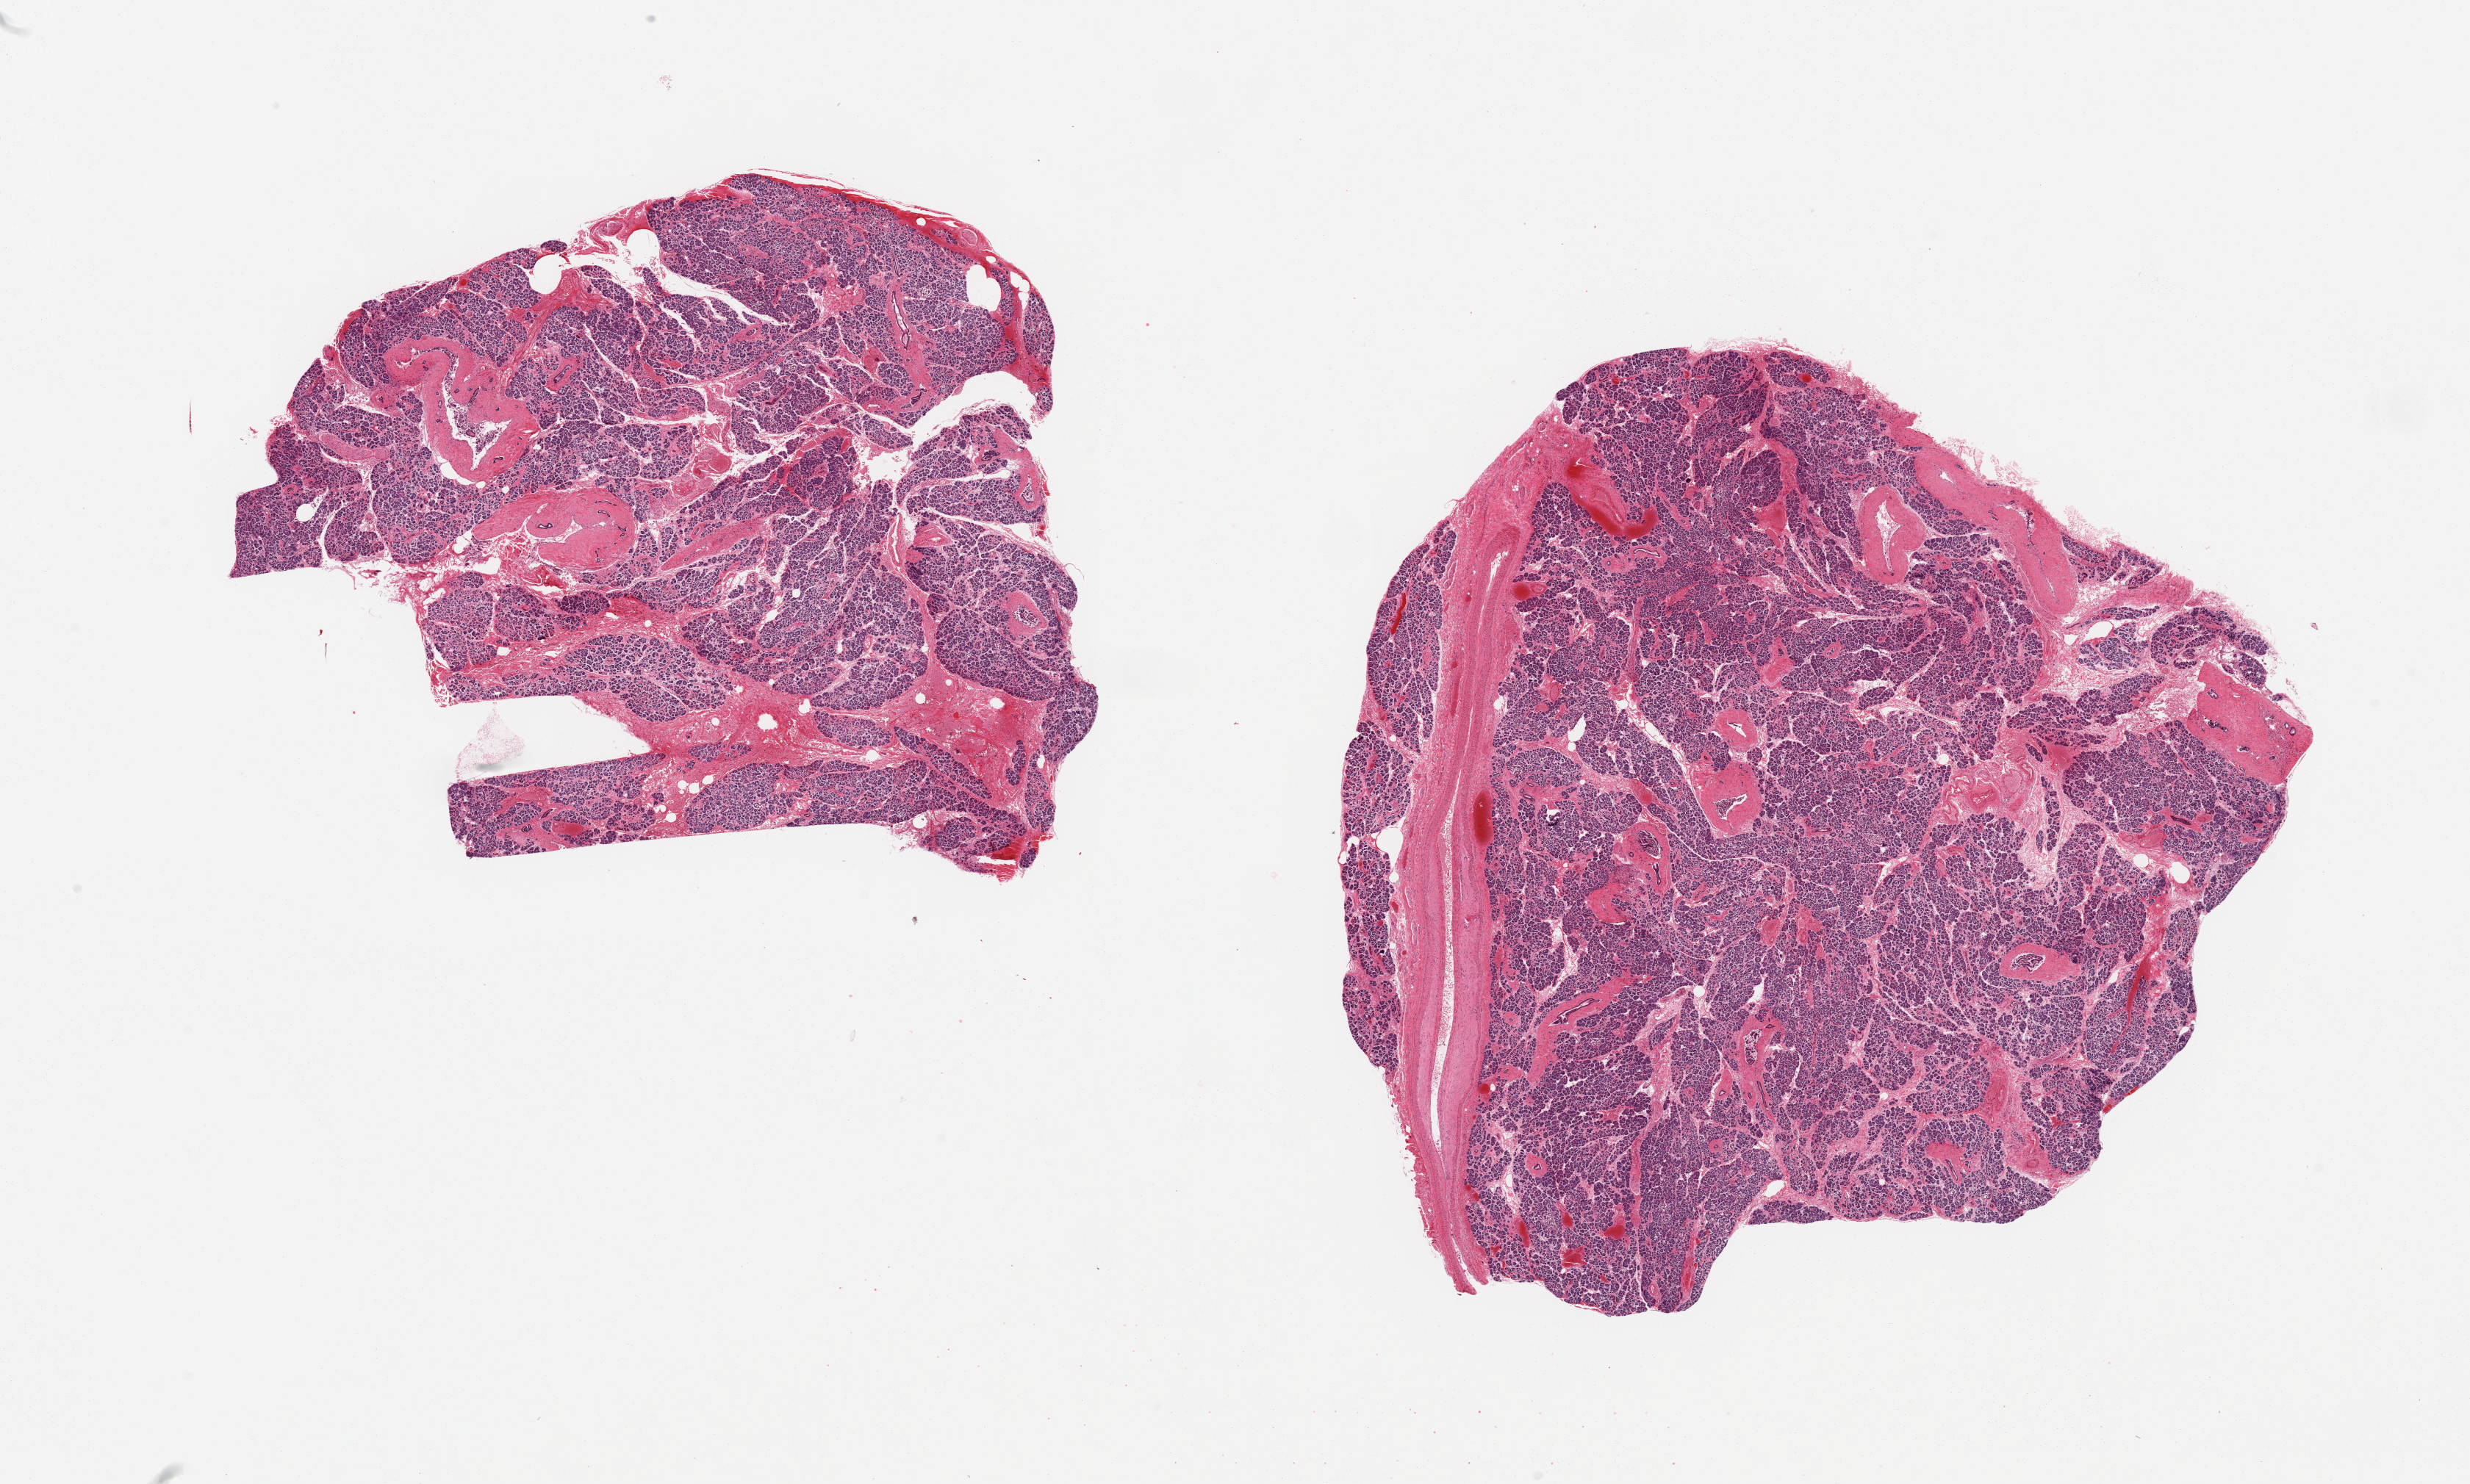
Digitized H&E-stained section — low-resolution overview of the scanned area, about 26.6 x 16.0 mm (slide scanned at 20x); PAXgene-fixed paraffin-embedded (PFPE) section; target tissue: pancreas; donor tissue sample.
* reviewer comment on this tissue sample: 2 pieces; congested thick fibrous septa; interstitial and periductal fibrosis; small sparsely cellular Langerhans islets